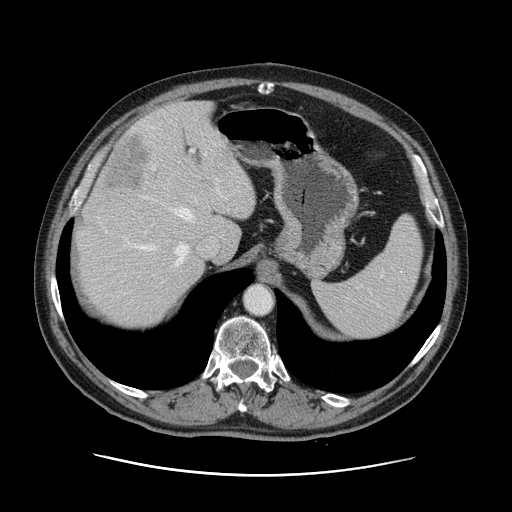
Contrast-enhanced abdominal CT, one axial slice; position 95 of 141 along the scan axis; intravenous contrast given; soft-tissue window (W 400 / L 40 HU); 2.5 mm slice thickness; 512 × 512 image matrix, field of view 395 × 395 mm. Male patient, age 72 years. From the clinical record (not read from this slice): diagnosis: colorectal cancer liver metastases, imaged before liver resection; multiple liver metastases: yes; largest metastasis: 5.4 cm; chemotherapy before resection: yes.
Structures marked on this image (expert manual segmentation):
- hepatic veins: bounding box (x1, y1, x2, y2) in pixels: (125, 154, 206, 265)
- liver: (73, 101, 256, 329)
- planned liver remnant (the part of the liver to remain after resection): (74, 101, 256, 329)
- portal vein (with intrahepatic branches): (124, 149, 221, 254)
- liver metastasis: (101, 132, 153, 192)